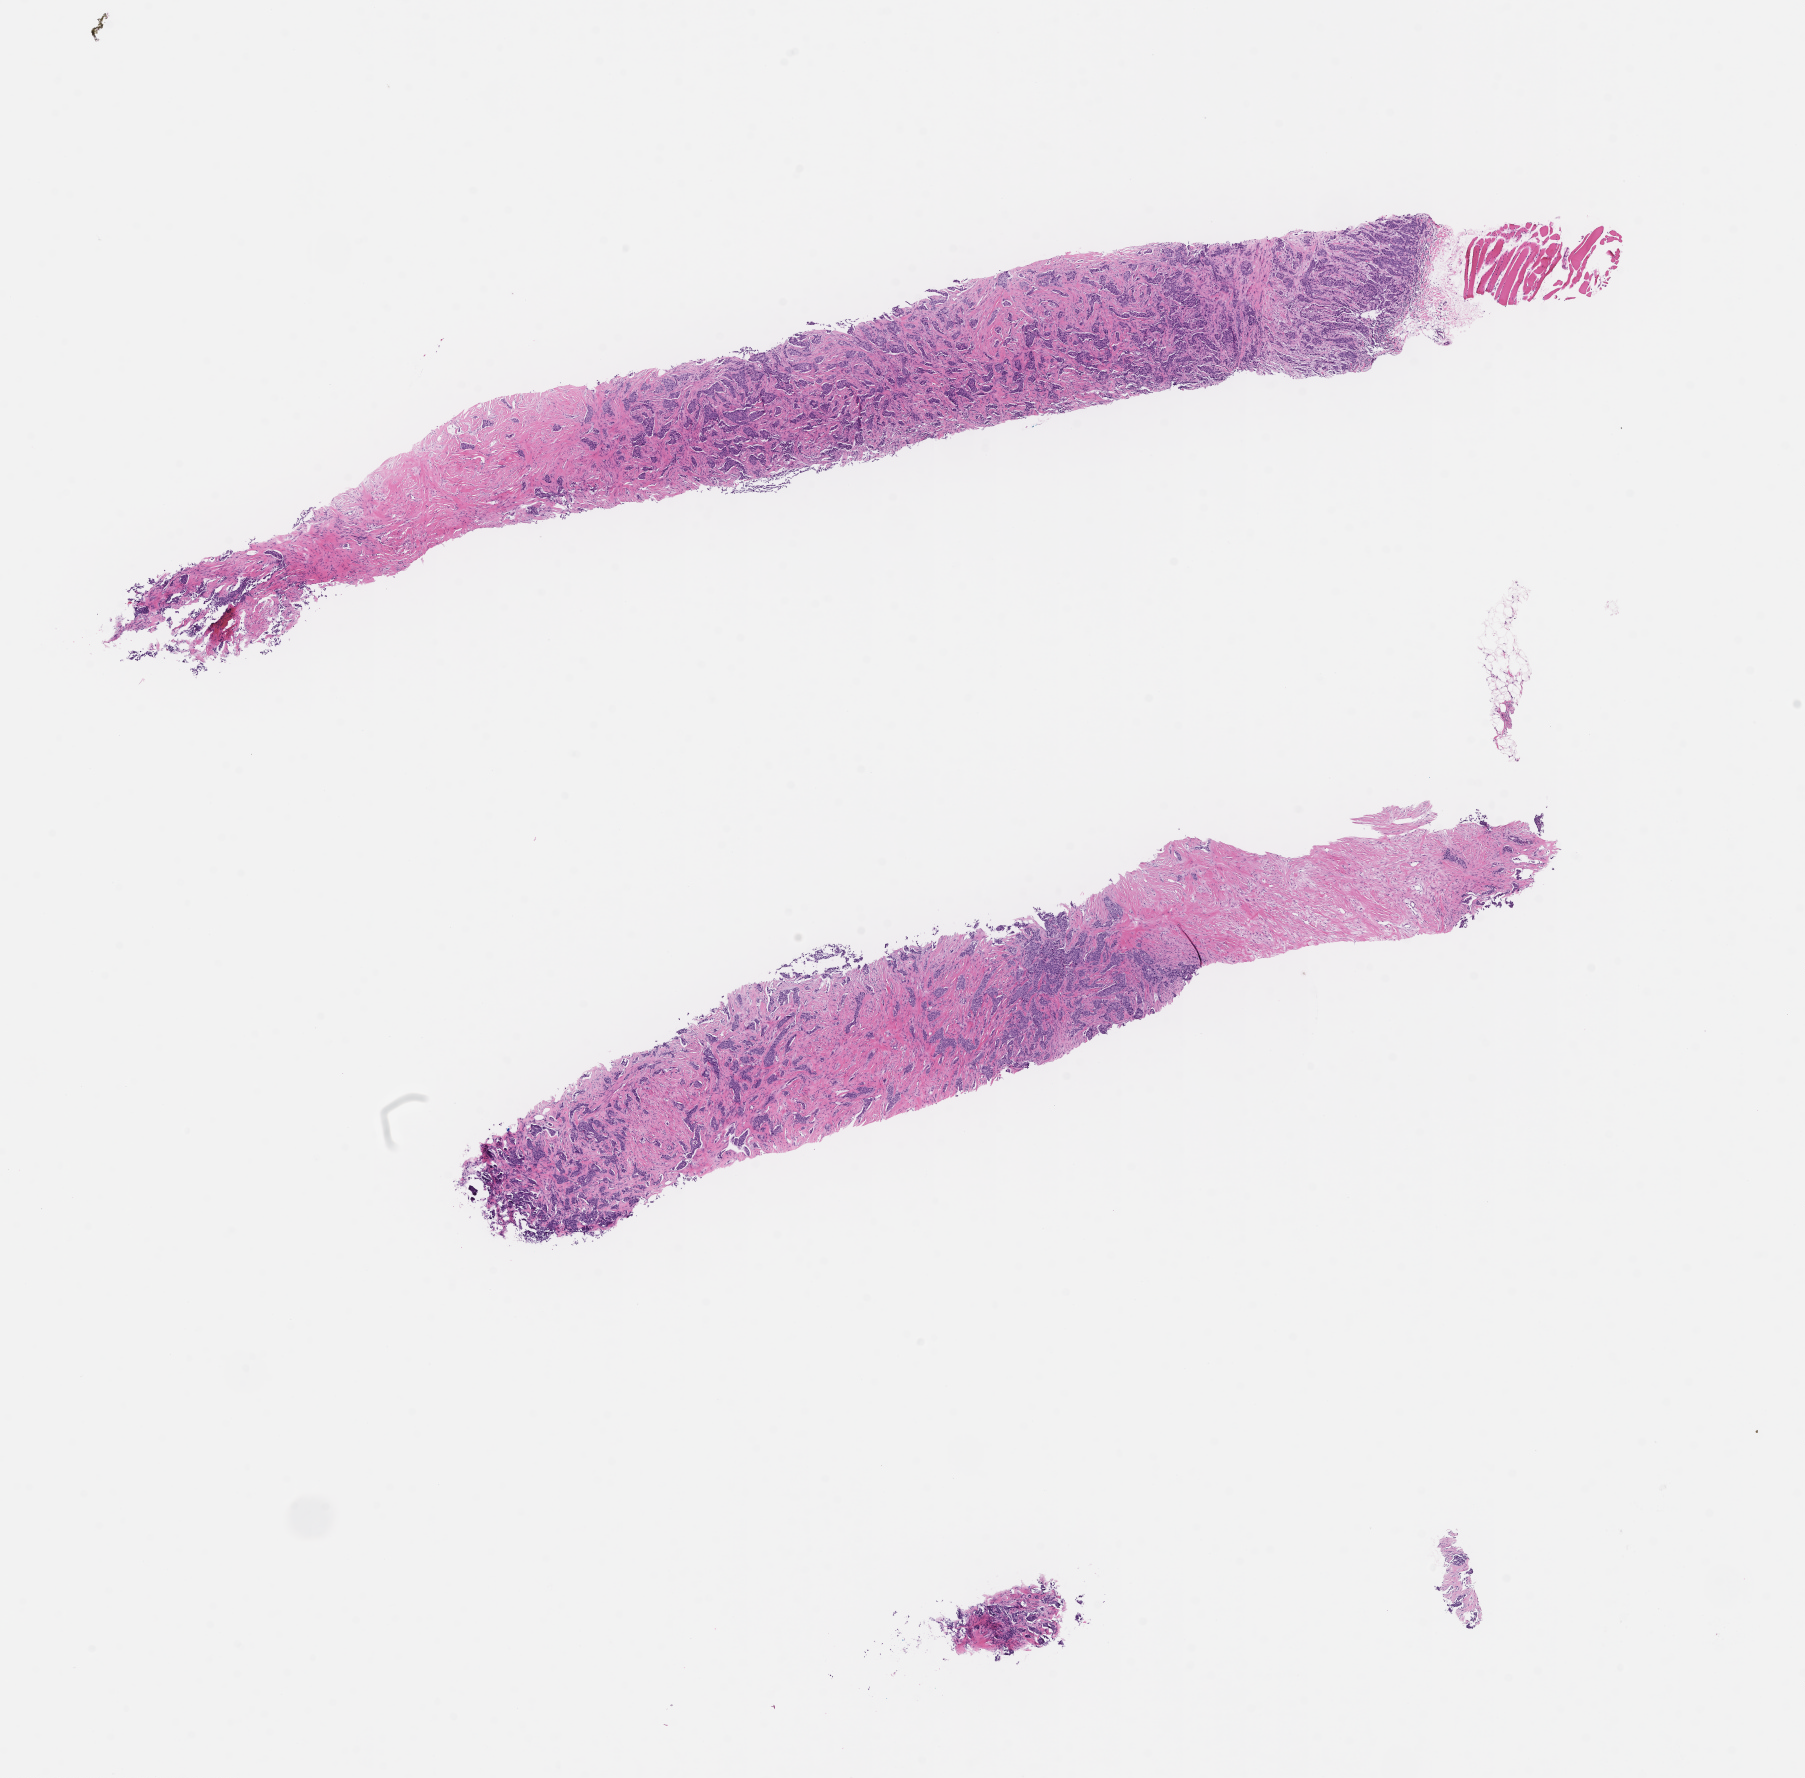
Hematoxylin and eosin (H&E) whole-slide image, low-resolution overview of the scanned area, about 14.6 x 14.4 mm, formalin-fixed, paraffin-embedded (FFPE) tissue, archival tissue. Female patient.
This section: metastasis (sampled organ not recorded). Patient diagnosis (primary): Invasive Breast Carcinoma.